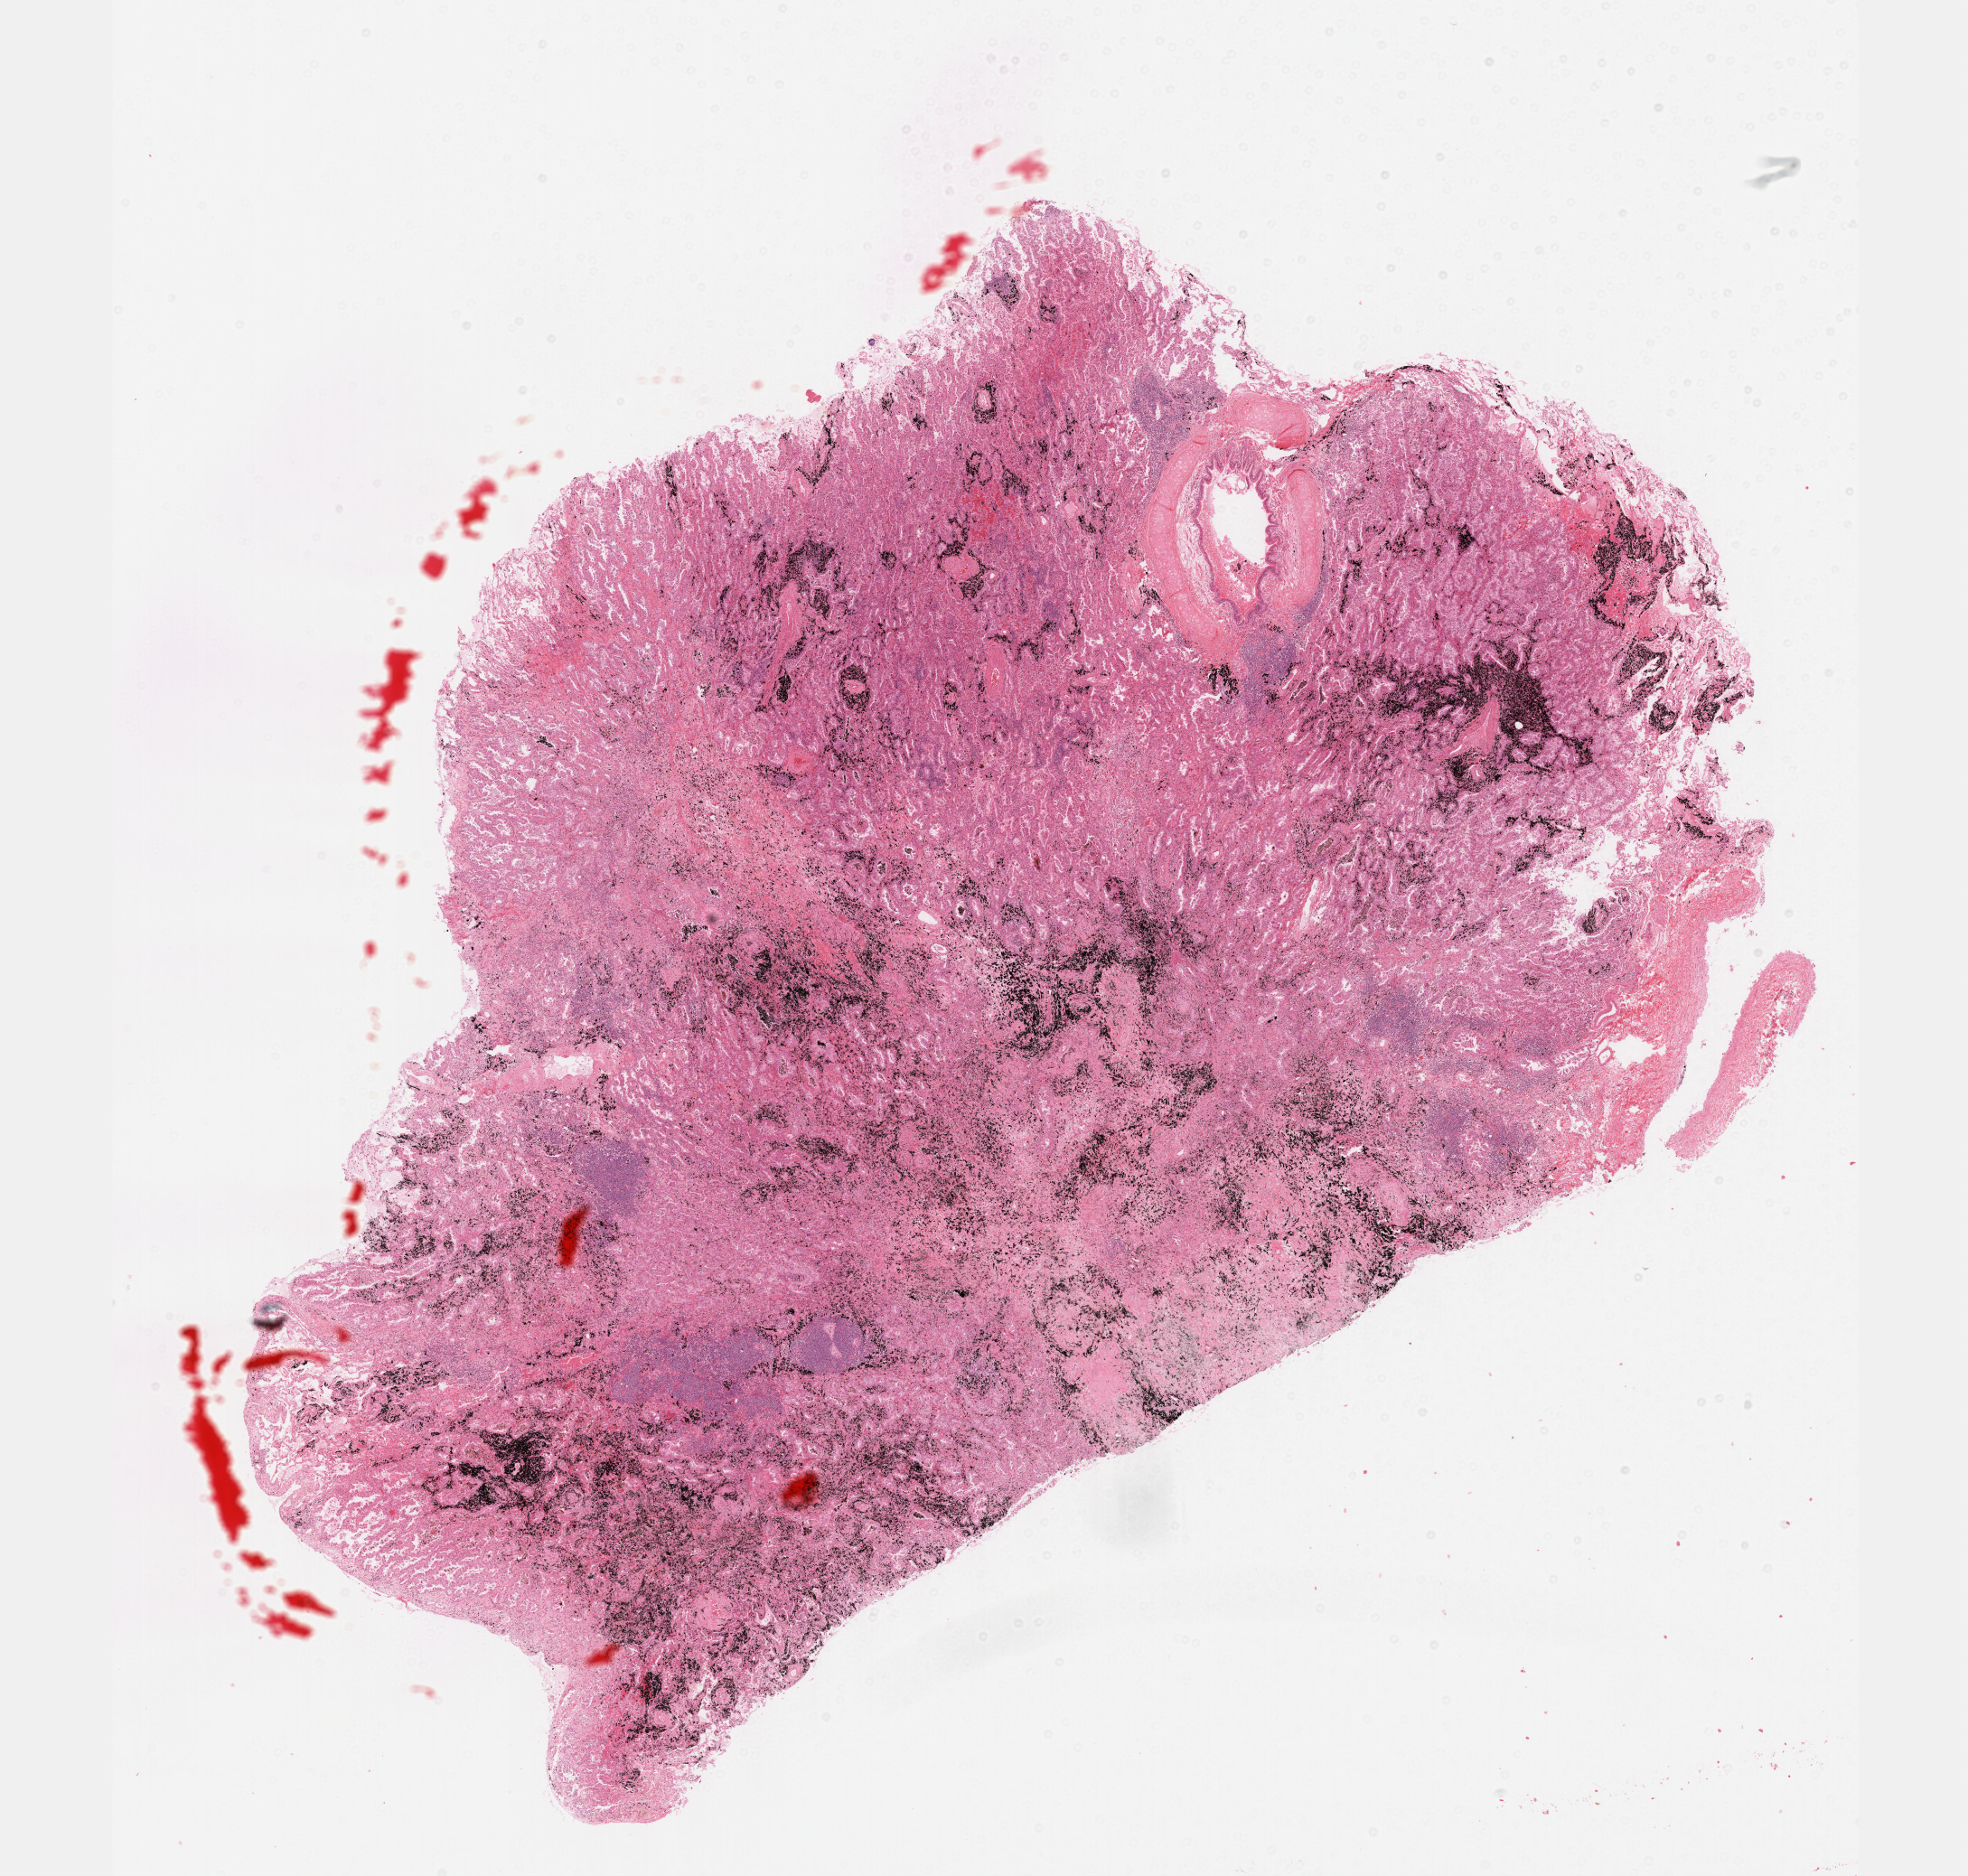
Whole-slide histology image, H&E-stained — low-resolution overview of the scanned area, about 17.6 x 16.8 mm (slide scanned at 40x), formalin-fixed paraffin-embedded (FFPE) diagnostic section, lung, primary tumour sample. Female patient; age at initial diagnosis 78 years.
AJCC pathologic stage: IA (7th edition). Pathologic diagnosis: Papillary adenocarcinoma, NOS. Laterality: left.